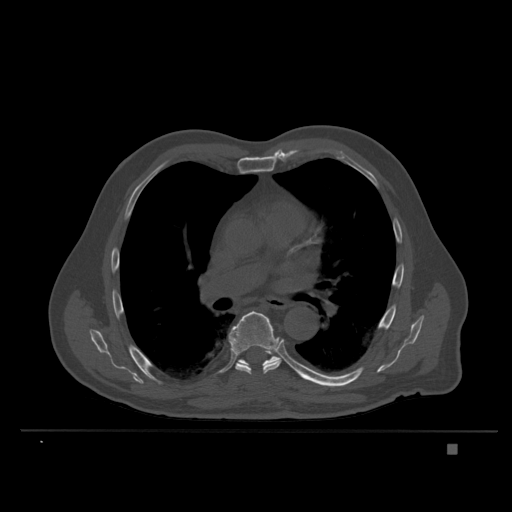
CT including the spine, one axial slice; position 241 of 435 along the scan axis; bone window (W 1800 / L 400 HU); 1.5 mm slice thickness; 512 × 512 image matrix. Patient: male, 73 years. From the clinical record (not read from this slice): primary cancer: skin.
Annotated regions visible in this slice (semi-automatic segmentation, software-assisted and operator-edited):
- T7 vertebra: box from (x=228, y=311) to (x=282, y=375) px
- T8 vertebra: (x=238, y=352)–(x=282, y=367)